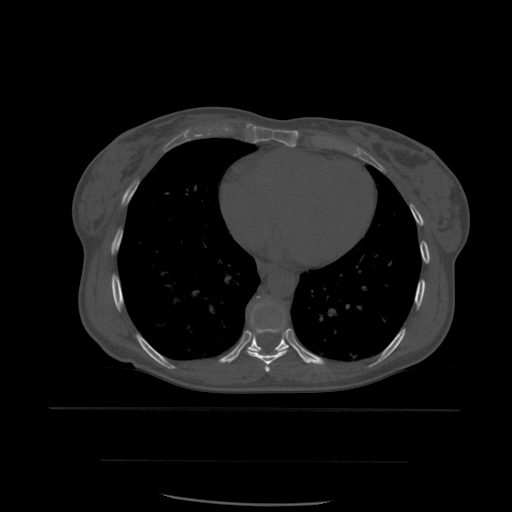
CT including the spine, one axial slice; slice 348 of 574 in the series (ordered by position); bone window (W 1800 / L 400 HU); 512 × 512 image matrix, field of view 392 × 392 mm. Patient age 48 years. From the clinical record (not read from this slice): primary cancer: lung.
Structures marked on this image (semi-automatic segmentation, software-assisted and operator-edited):
- T7 vertebra: bounding box <266,367,270,372> (left, top, right, bottom; pixels)
- T8 vertebra: <247,296,289,373>
- T9 vertebra: <231,300,314,364>